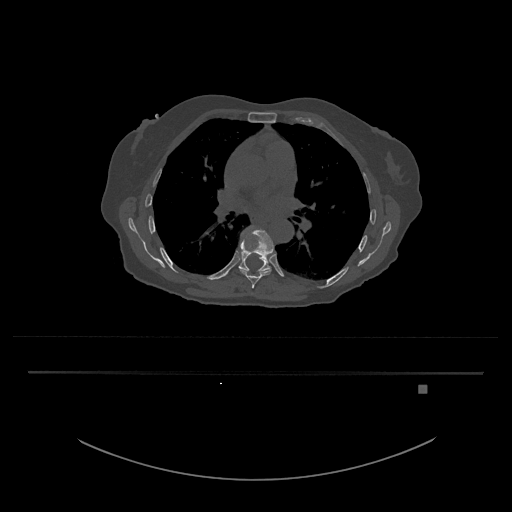
CT including the spine, one axial slice; position 785 of 797 along the scan axis; 120 kVp; bone window (W 1800 / L 400 HU); 512 × 512 image matrix, field of view 500 × 500 mm. Female patient, age 57 years. Case-level facts recorded for this patient, not image findings: primary cancer: cervical.
Annotated regions visible in this slice (semi-automatically segmented with operator editing):
- T8 vertebra: bounding box <238,226,274,289> (left, top, right, bottom; pixels)
- T9 vertebra: <236,236,271,273>